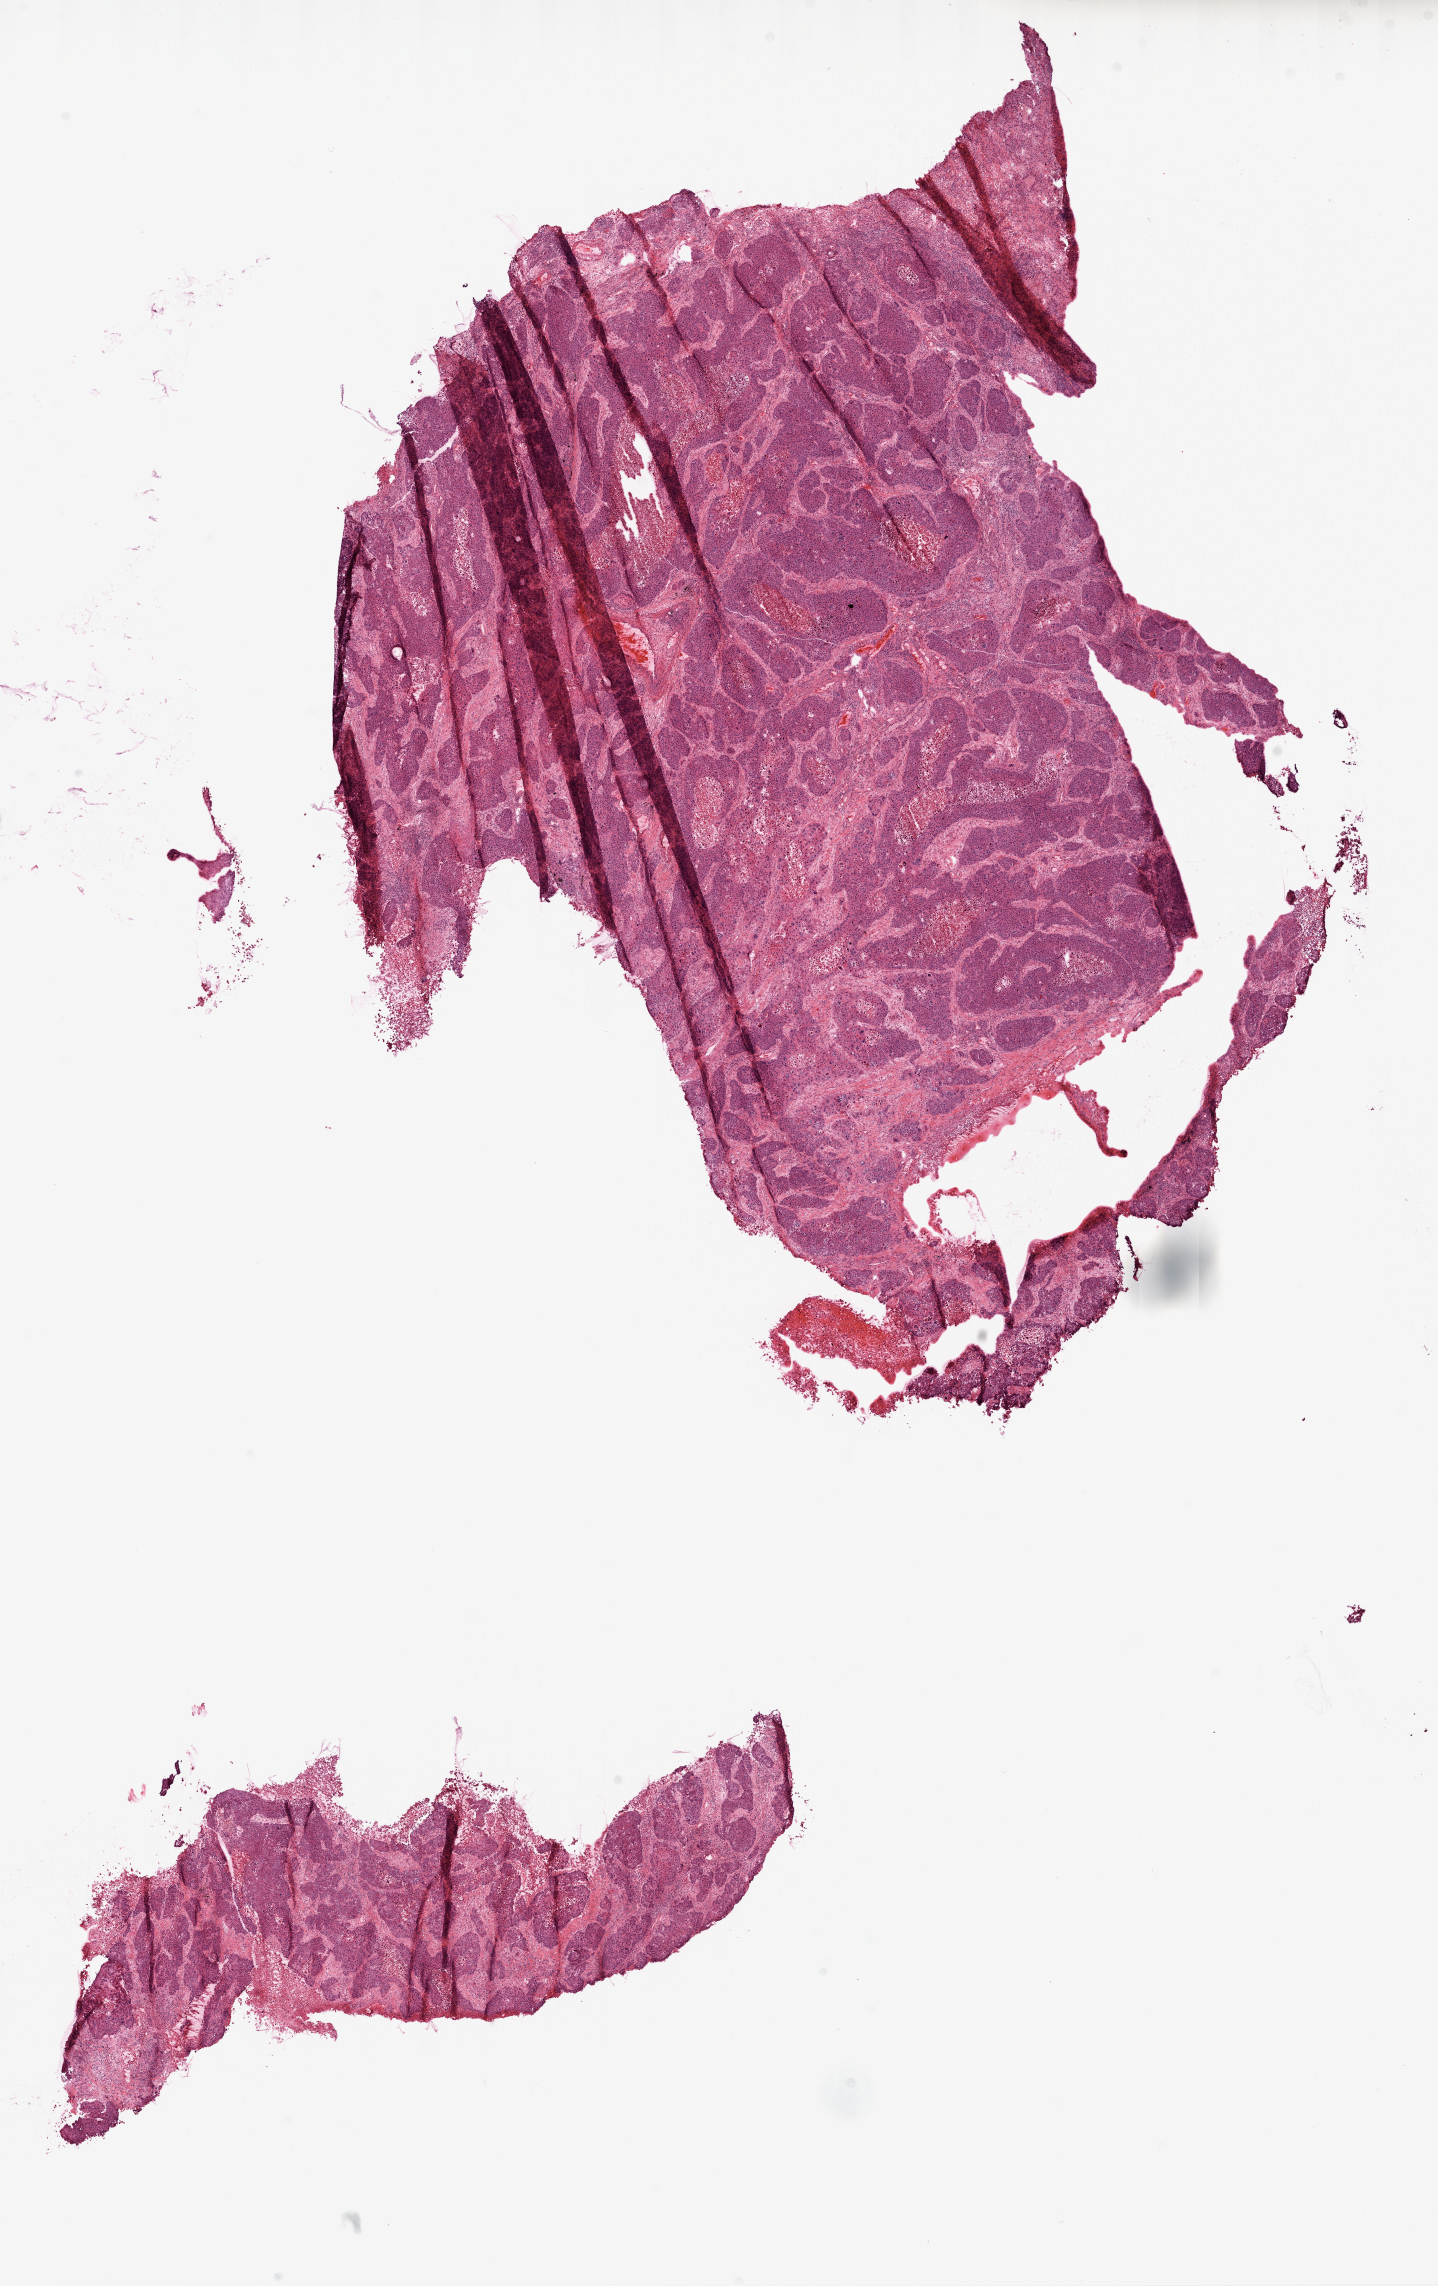
Hematoxylin and eosin (H&E) stained whole-slide image, shown as a low-resolution overview of the whole scanned area (about 11.6 x 18.4 mm, from a 20x scan). Frozen section from the top of the tissue portion. Primary tumour sample from the lung. Male patient; age at initial diagnosis 66 years. Slide review estimates, as recorded: tumour nuclei 95%, necrosis 0%.
TNM: T2 N0 M0. AJCC pathologic stage: IB. Diagnosis: Squamous cell carcinoma, NOS (lower lobe, lung).